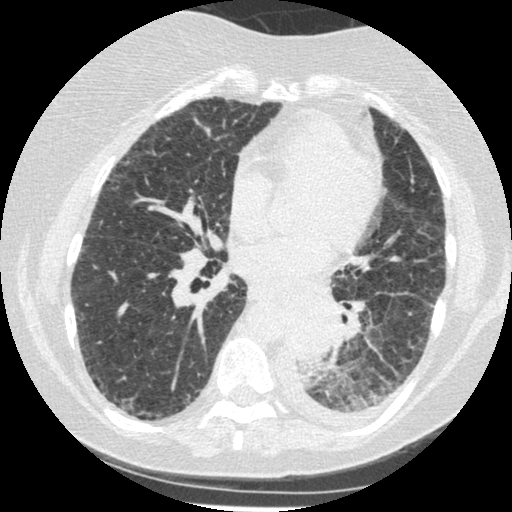
Low-dose screening chest CT, one axial slice. Position 104 of 341 along the scan axis. 120 kVp. Lung window (W 1500 / L -600 HU). 512 × 512 image matrix.
Annotated regions visible in this slice (expert manual segmentation):
- lesion 1 (tumor, lower lobe of left lung): box from (x=285, y=304) to (x=339, y=364) px